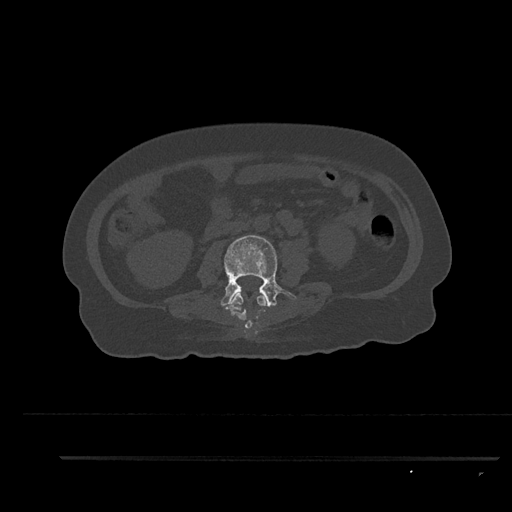
CT including the spine, one axial slice; position 107 of 797 along the scan axis; reconstruction kernel Br40s/3; bone window (W 1800 / L 400 HU); 512 × 512 image matrix, field of view 408 × 408 mm. Patient: female, 44 years. Case-level facts recorded for this patient, not image findings: primary cancer: renal; vertebrae with lytic lesions (as recorded): L1.
Outlined on this slice (semi-automatically segmented with operator editing):
- L2 vertebra: bounding box (x1, y1, x2, y2) in pixels: (226, 293, 266, 329)
- L3 vertebra: (220, 235, 296, 312)